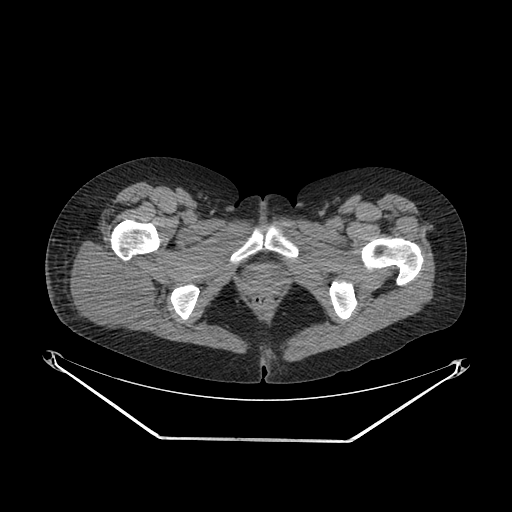
CT of an extremity soft-tissue mass (from a PET/CT study), one axial slice. Position 40 of 267 along the scan axis. Soft-tissue window (W 400 / L 40 HU). 512 × 512 image matrix, field of view 500 × 500 mm. Female patient. Case-level facts recorded for this patient, not image findings: histological type: epithelioid sarcoma with vascular differentiation; site of the primary tumour: right buttock.
Outlined on this slice (expert contour drawn on MRI and transferred to this co-registered scan by the dataset authors):
- gross tumour volume (mass): bounding box (x1, y1, x2, y2) in pixels: (66, 240, 156, 332)